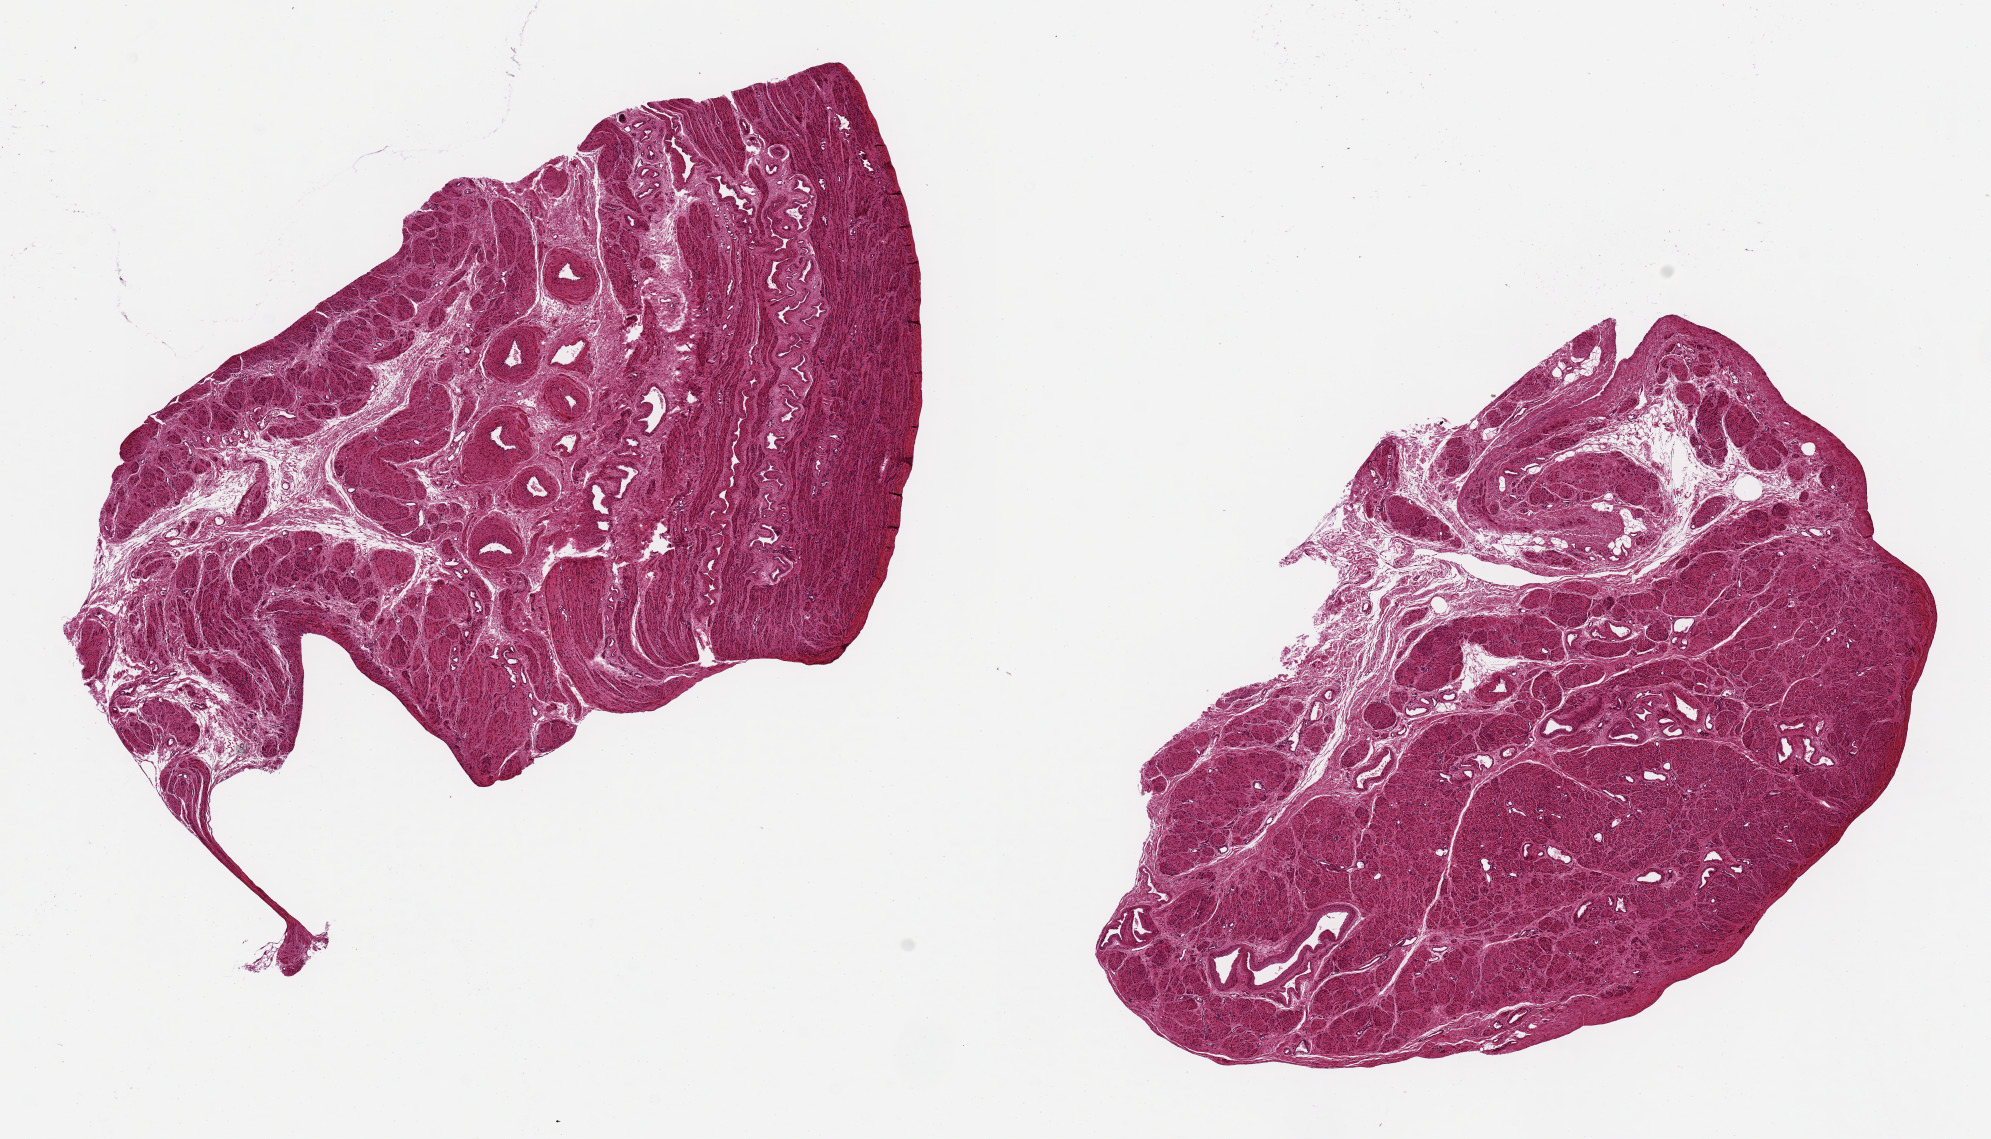
Digitized hematoxylin and eosin (H&E)-stained section — low-resolution overview of the scanned area, about 15.8 x 9.0 mm (slide scanned at 20x), PAXgene-fixed, paraffin-embedded tissue, section of fallopian tube (target tissue), tissue donor sample. Female donor.
- pathologist's review note for this sample: 2 pieces 7x4 mm; NO fallopian tube; only smooth muscle, vessels and stroma